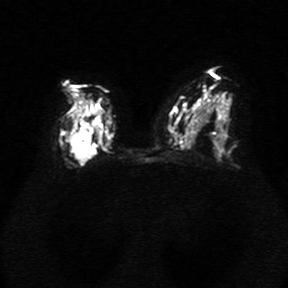
Breast MRI, one axial slice; slice 17 of 34 in the series (ordered by position); diffusion-weighted series; image 2 of 4 stored at this slice position (different b-values; order by instance number); 1.5 T; 5 mm slice thickness; 288 × 288 image matrix, field of view 340 × 340 mm. Female patient.
Structures marked on this image (expert manual segmentation):
- tumour on diffusion-weighted imaging: bounding box [x1, y1, x2, y2] px = [69, 116, 103, 164]